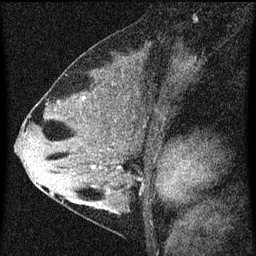
Breast MRI (dynamic contrast-enhanced), one sagittal slice; position 35 of 60 along the scan axis; dynamic contrast-enhanced series, image 2 of 3 at this slice position (ordered by acquisition); 1.5 T; TE 4.2 ms, TR 8 ms; 2 mm slice thickness; 256 × 256 image matrix, field of view 180 × 180 mm. Patient: female, 33 years.
Structures marked on this image (semi-automatically segmented with operator editing):
- analysis volume of interest (the breast-tissue region the enhancement analysis was run in; not a lesion): bounding box (x1, y1, x2, y2) in pixels: (67, 118, 160, 215)
- tumour enhancement mask (voxels above the 70 % enhancement threshold inside the analysis volume of interest): (91, 166, 94, 169)